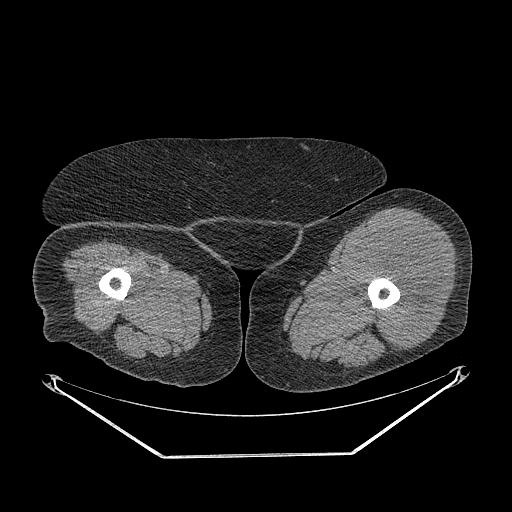
CT of an extremity soft-tissue mass (from a PET/CT study), one axial slice; reconstruction kernel STANDARD; 140 kVp; soft-tissue window (W 400 / L 40 HU); 512 × 512 image matrix, field of view 500 × 500 mm. Female patient. Case-level facts recorded for this patient, not image findings: histological type: undifferentiated – high grade; grade: high; site of the primary tumour: left thigh.
Annotated regions visible in this slice (expert contour drawn on MRI and transferred to this co-registered scan by the dataset authors):
- gross tumour volume including surrounding oedema: box from (x=352, y=226) to (x=444, y=350) px
- gross tumour volume (mass): (x=352, y=226)–(x=444, y=350)